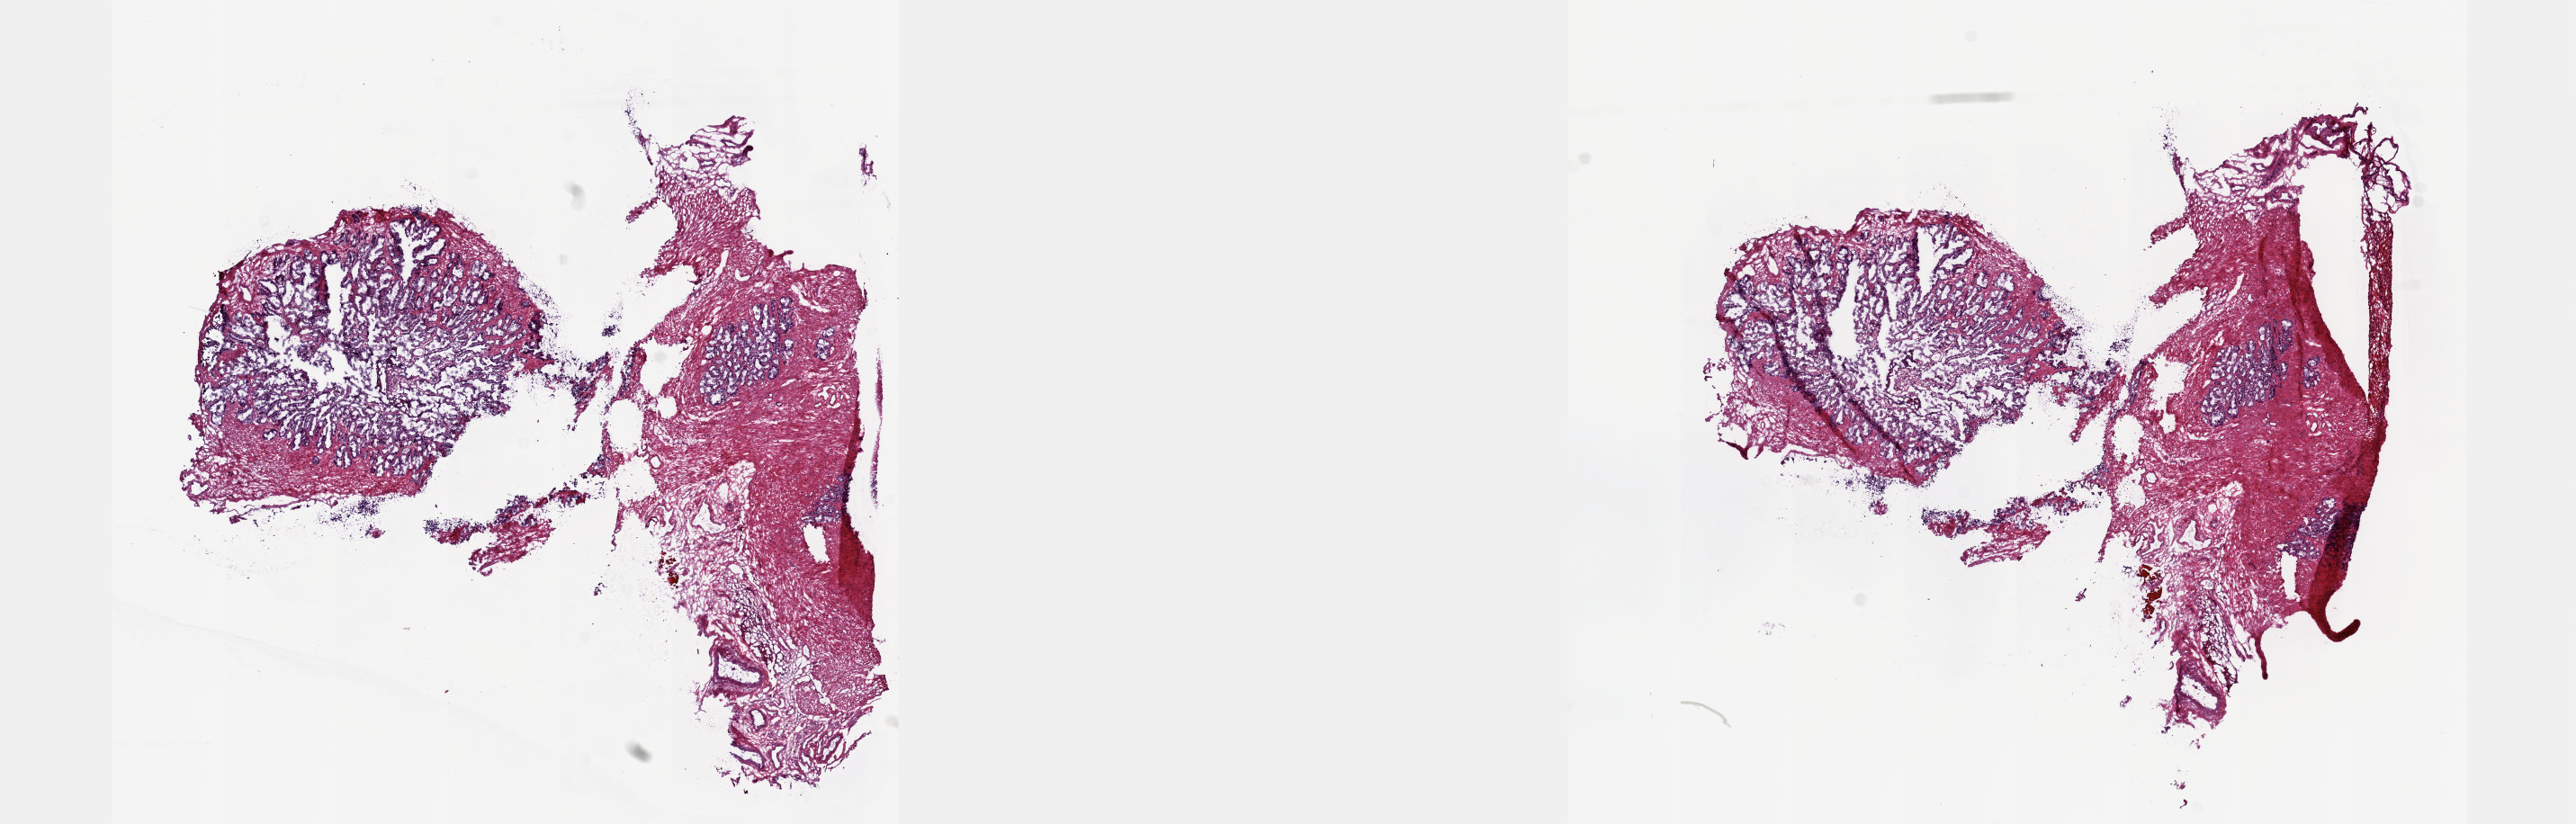
Whole-slide histology image, H&E-stained — shown as a low-resolution overview of the whole scanned area (about 23.1 x 7.4 mm); frozen section from the top of the tissue portion; sample: solid tissue normal (non-tumour tissue), prostate. Male, age 55 years at initial diagnosis. Pathologist review of this section (percent, as recorded): tumour cells 0%, tumour nuclei 0%, normal cells 35%, stromal cells 65%, necrosis 0%. Infiltration values recorded for this section: lymphocyte infiltration 3%, monocyte infiltration 0%, neutrophil infiltration 0%.
This section: solid tissue normal sample (biorepository sample class). Patient diagnosis: Adenocarcinoma, NOS (prostate gland).